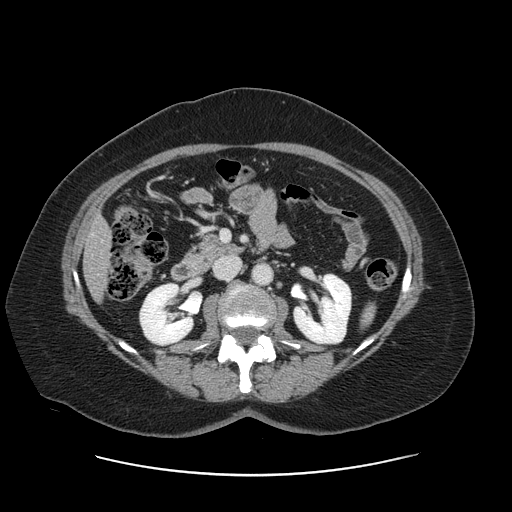
Contrast-enhanced abdominal CT, one axial slice. Position 51 of 161 along the scan axis. 120 kVp. Intravenous contrast given. Soft-tissue window (W 400 / L 40 HU). 2.5 mm slice thickness. 512 × 512 image matrix, field of view 398 × 398 mm. Female patient, age 62 years. Case-level facts recorded for this patient, not image findings: diagnosis: colorectal cancer liver metastases, imaged before liver resection; multiple liver metastases: no; largest metastasis: 2.5 cm; disease in both lobes: no.
Outlined on this slice (outlined manually by an expert reader):
- liver: bounding box (x1, y1, x2, y2) in pixels: (85, 218, 110, 297)